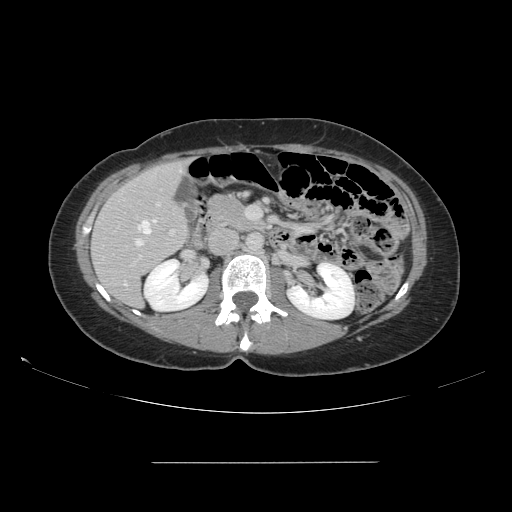
Contrast-enhanced abdominal CT, one axial slice. Slice 73 of 151 in the series (ordered by position). 120 kVp. Intravenous contrast given. Soft-tissue window (W 400 / L 40 HU). 2.5 mm slice thickness. 512 × 512 image matrix, field of view 421 × 421 mm. Female patient, age 46 years. From the clinical record (not read from this slice): diagnosis: colorectal cancer liver metastases, imaged before liver resection; multiple liver metastases: yes; largest metastasis: 3 cm.
Structures marked on this image (expert manual segmentation):
- hepatic veins: bounding box <135,219,156,246> (left, top, right, bottom; pixels)
- liver: <93,162,188,307>
- planned liver remnant (the part of the liver to remain after resection): <93,162,187,307>
- portal vein (with intrahepatic branches): <131,202,175,266>